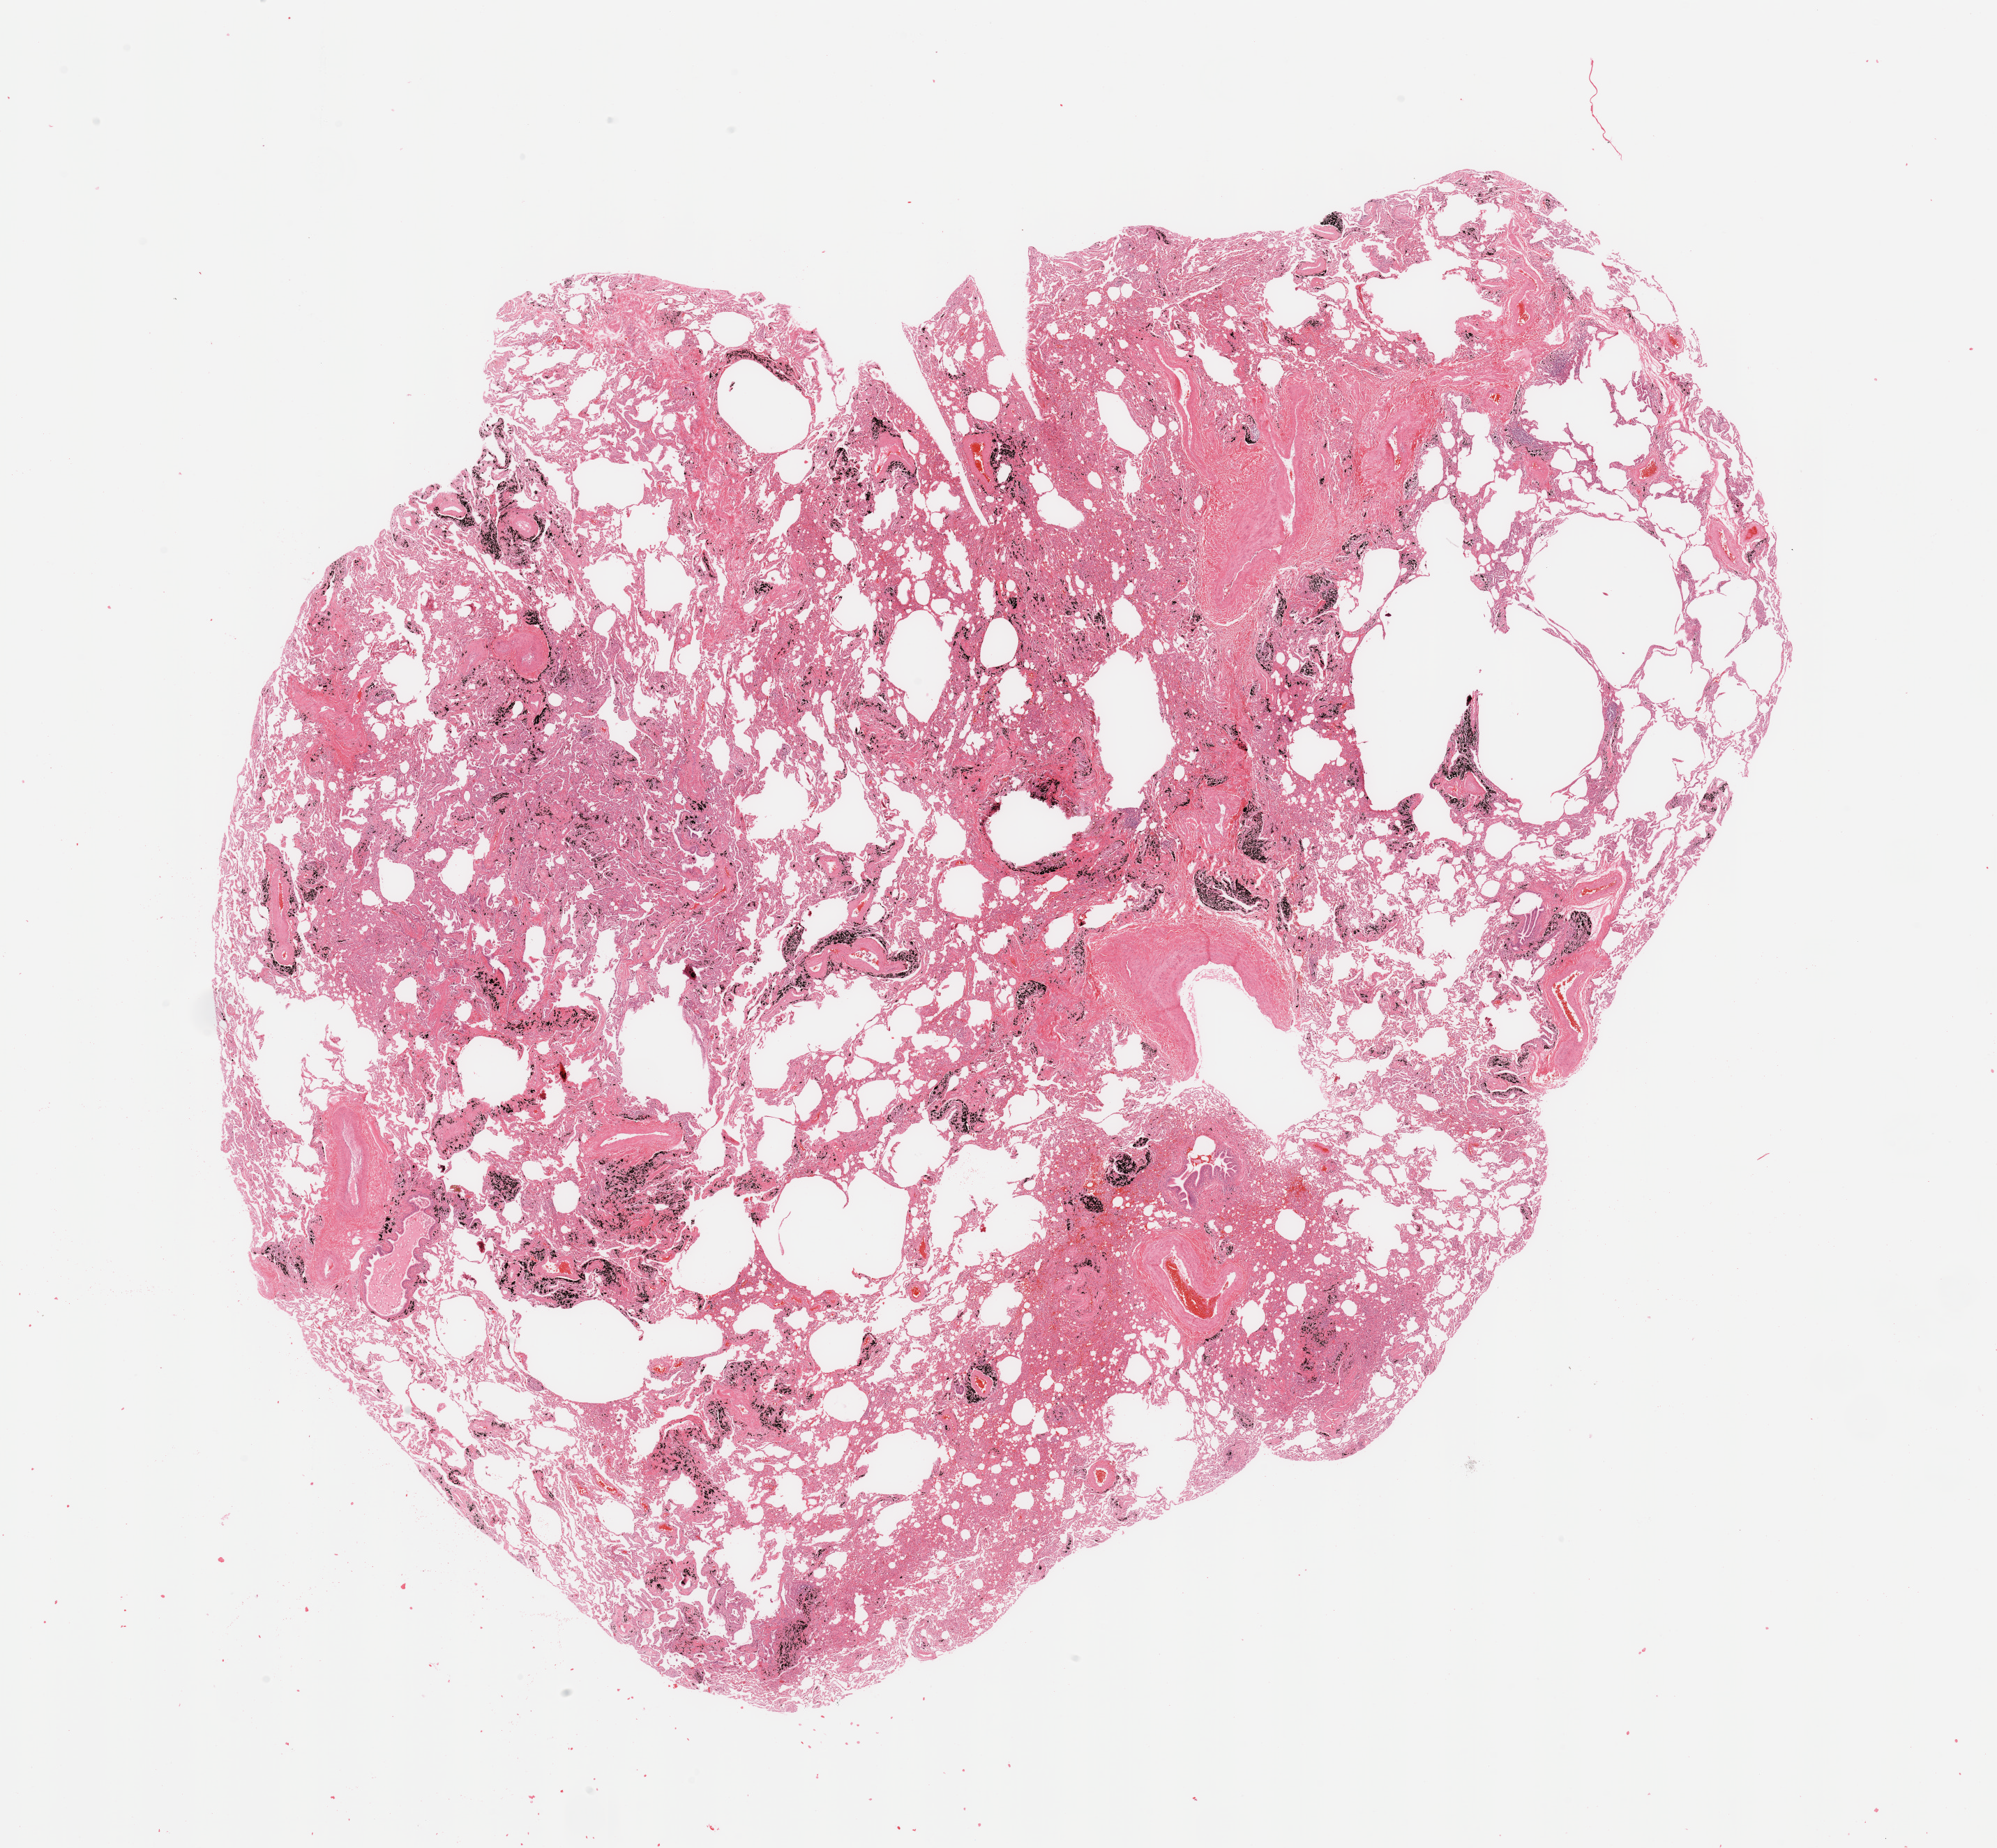
Hematoxylin and eosin (H&E) stained whole-slide image — shown as a low-resolution overview of the whole scanned area (about 22.6 x 20.9 mm). Normal (non-tumour) tissue sample, sampled site: lung. 72-year-old male patient.
* this section: normal (non-tumour) tissue from the same patient
* patient diagnosis: Squamous cell carcinoma, NOS